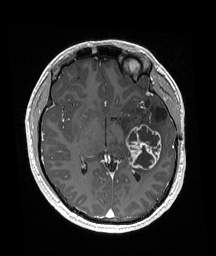
Brain MRI from a brain-tumour surgery series, one axial slice. Slice 97 of 192 in the series (ordered by position). T1-weighted post-contrast. 1 mm slice thickness. 216 × 256 image matrix. Case-level facts recorded for this patient, not image findings: histopathology: Glioneuronal tumor; WHO grade: 2; tumour location: Left Superior Temporal Gyrus.
Outlined on this slice (manually delineated by an expert):
- previous resection cavity: bounding box <156,108,167,121> (left, top, right, bottom; pixels)
- tumour: <127,124,162,170>